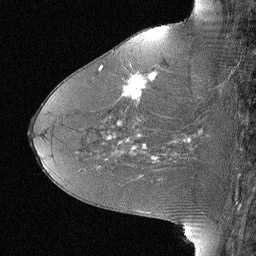
Breast MRI (dynamic contrast-enhanced), one sagittal slice. Slice 30 of 64 in the series (ordered by position). Dynamic contrast-enhanced study with each time point stored as its own series, time point 2 of 3 at this slice position (early post-contrast, ordered by acquisition time). 1.5 T. TE 4 ms, TR 30 ms. 2.25 mm slice thickness. 256 × 256 image matrix, field of view 180 × 180 mm. Female patient, age 46 years. From the clinical record (not read from this slice): setting: breast cancer imaged before/during neoadjuvant chemotherapy; receptor status: HR-positive, HER2-negative.
Annotated regions visible in this slice (semi-automatic segmentation, software-assisted and operator-edited):
- analysis volume of interest (the breast-tissue region the enhancement analysis was run in; not a lesion): bounding box <106,43,184,119> (left, top, right, bottom; pixels)
- tumour enhancement mask (voxels above the 90 % enhancement threshold inside the analysis volume of interest): <123,72,157,100>